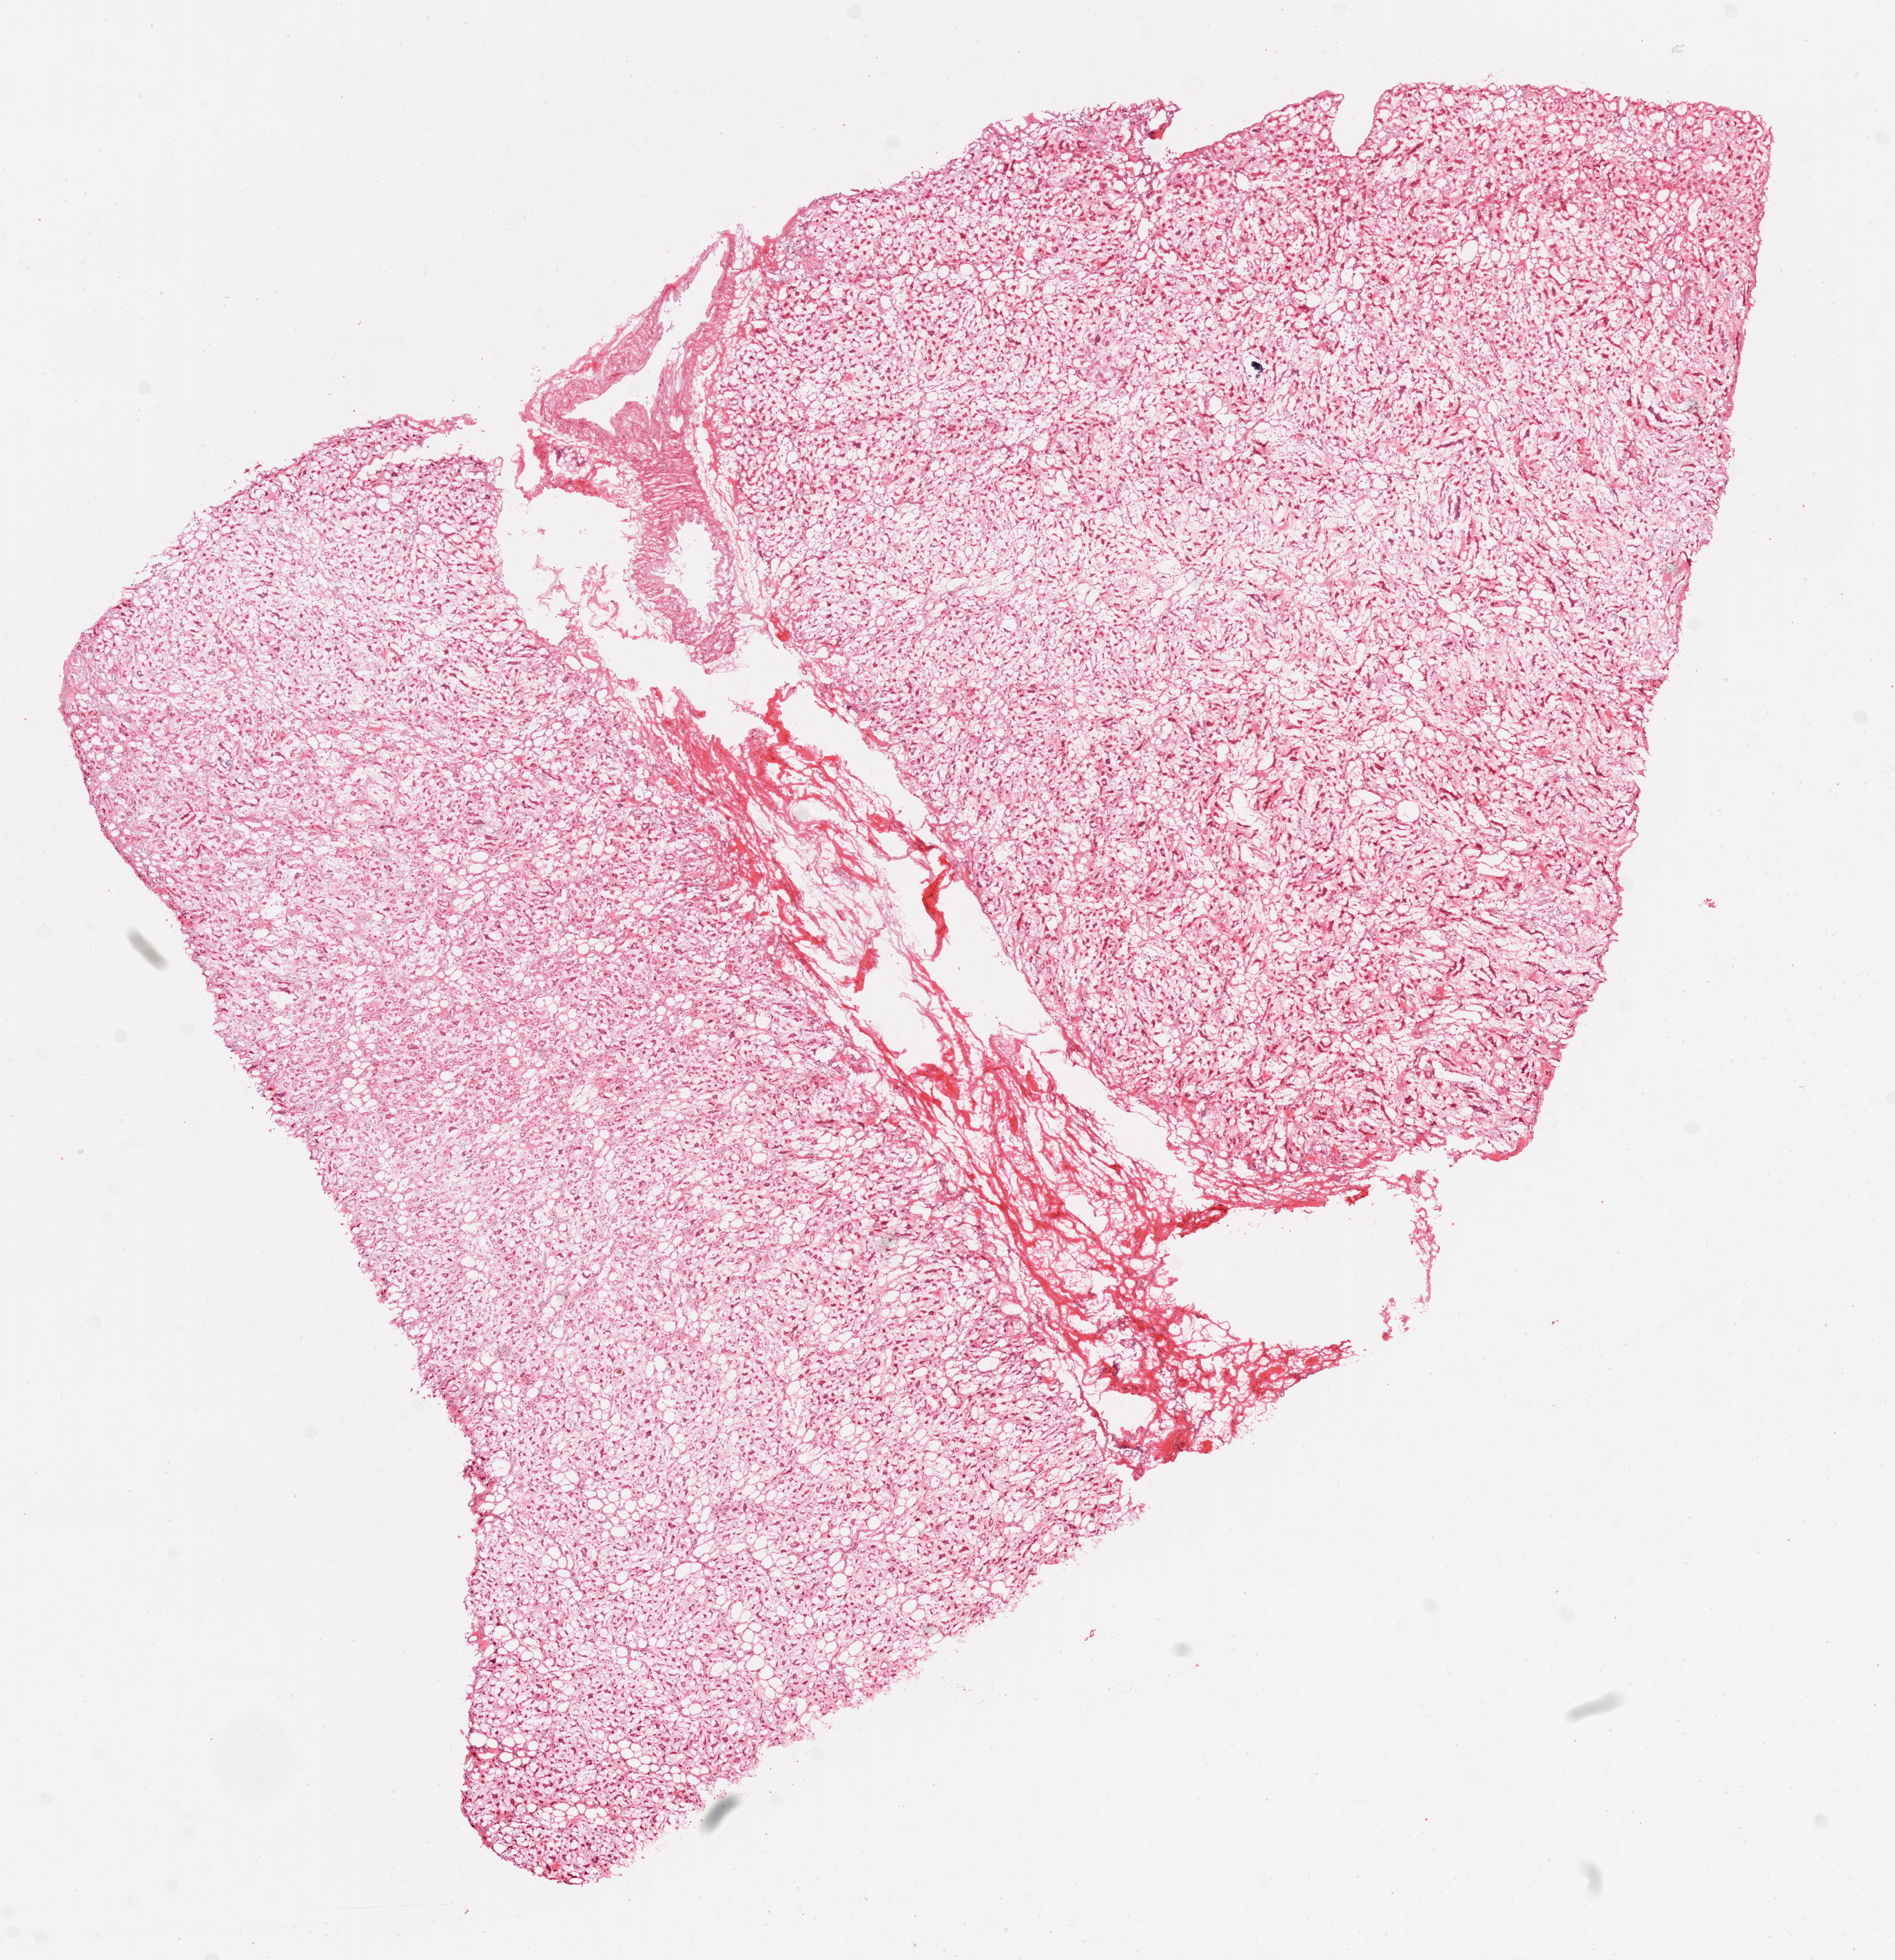
Hematoxylin and eosin (H&E) stained whole-slide image, whole scanned area (about 11.0 x 11.4 mm, from a 20x scan) shown as a low-resolution overview, frozen section from the top of the tissue portion, kidney, solid tissue normal (non-tumour tissue) sample. Female, age 72 years at initial diagnosis.
* this section: solid tissue normal sample (biorepository sample class)
* patient diagnosis: Clear cell adenocarcinoma, NOS